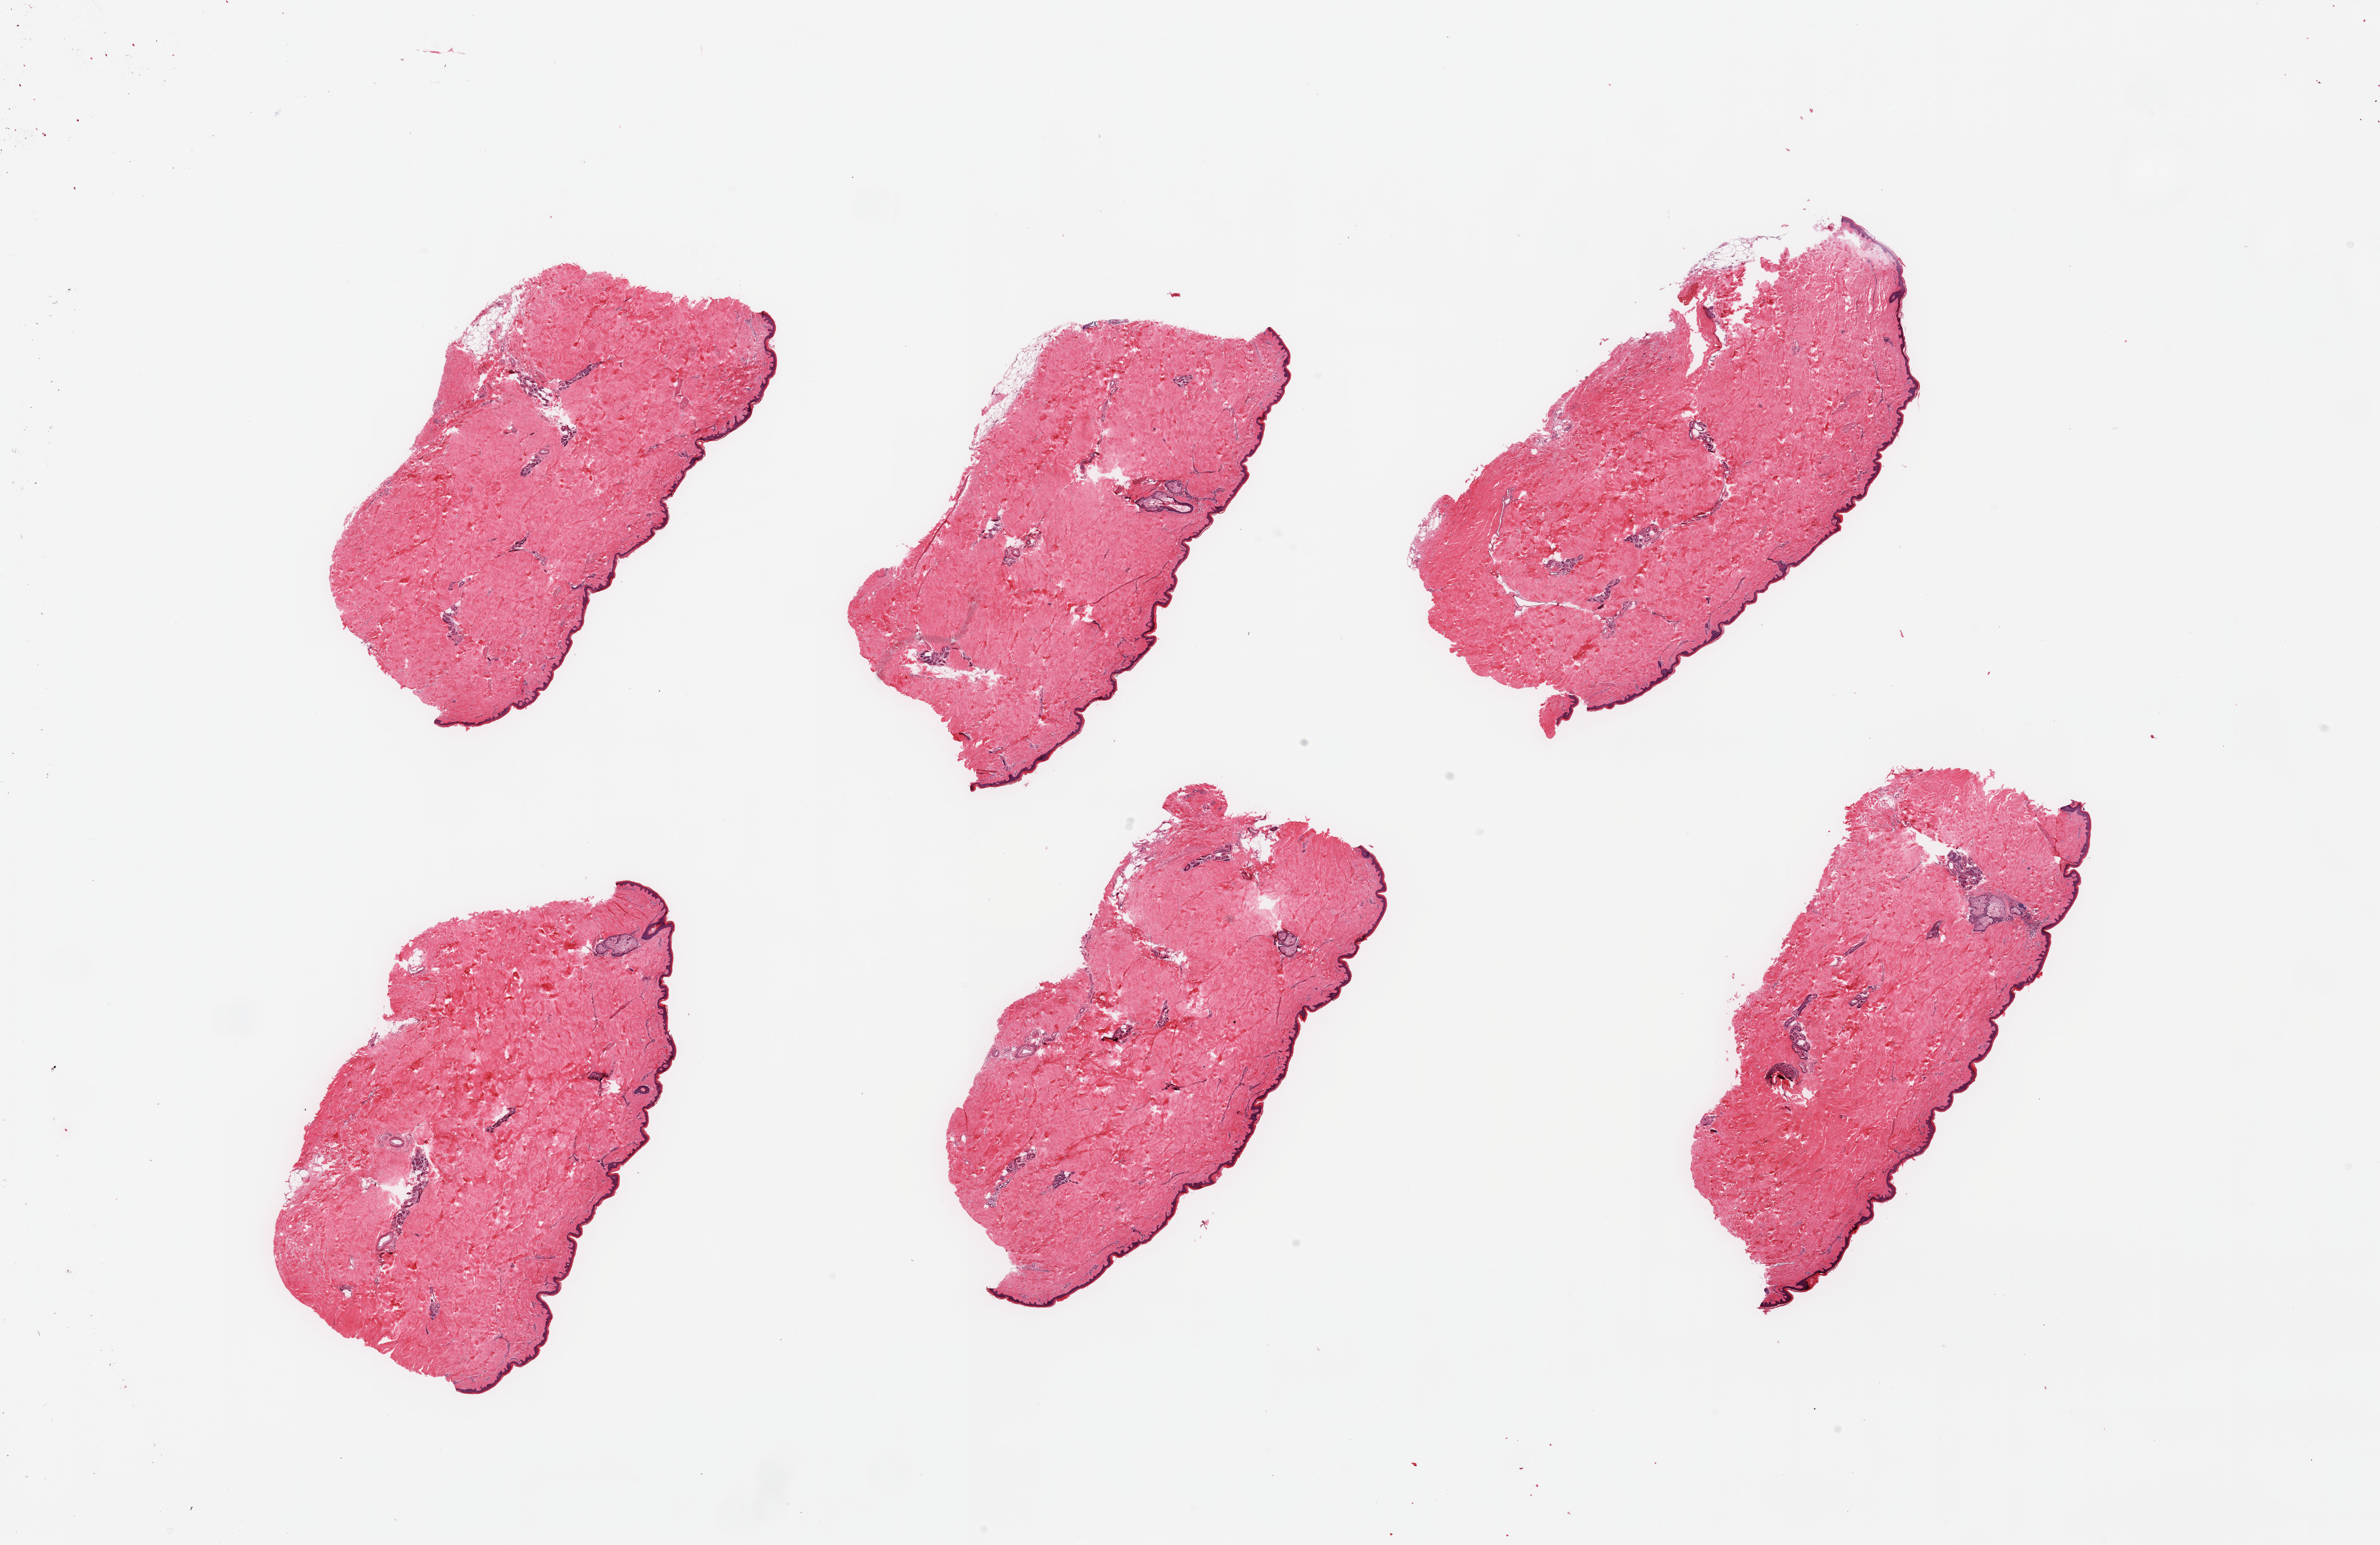
Hematoxylin and eosin (H&E) whole-slide image — shown as a low-resolution overview of the whole scanned area (about 31.5 x 20.4 mm, slide scanned at 20x); PAXgene-fixed paraffin-embedded (PFPE) section; target tissue: skin of lower leg; donor tissue sample. Male donor.
Reviewer comment on this tissue sample: 6 pieces; well trimmed; <2% dermal fat.